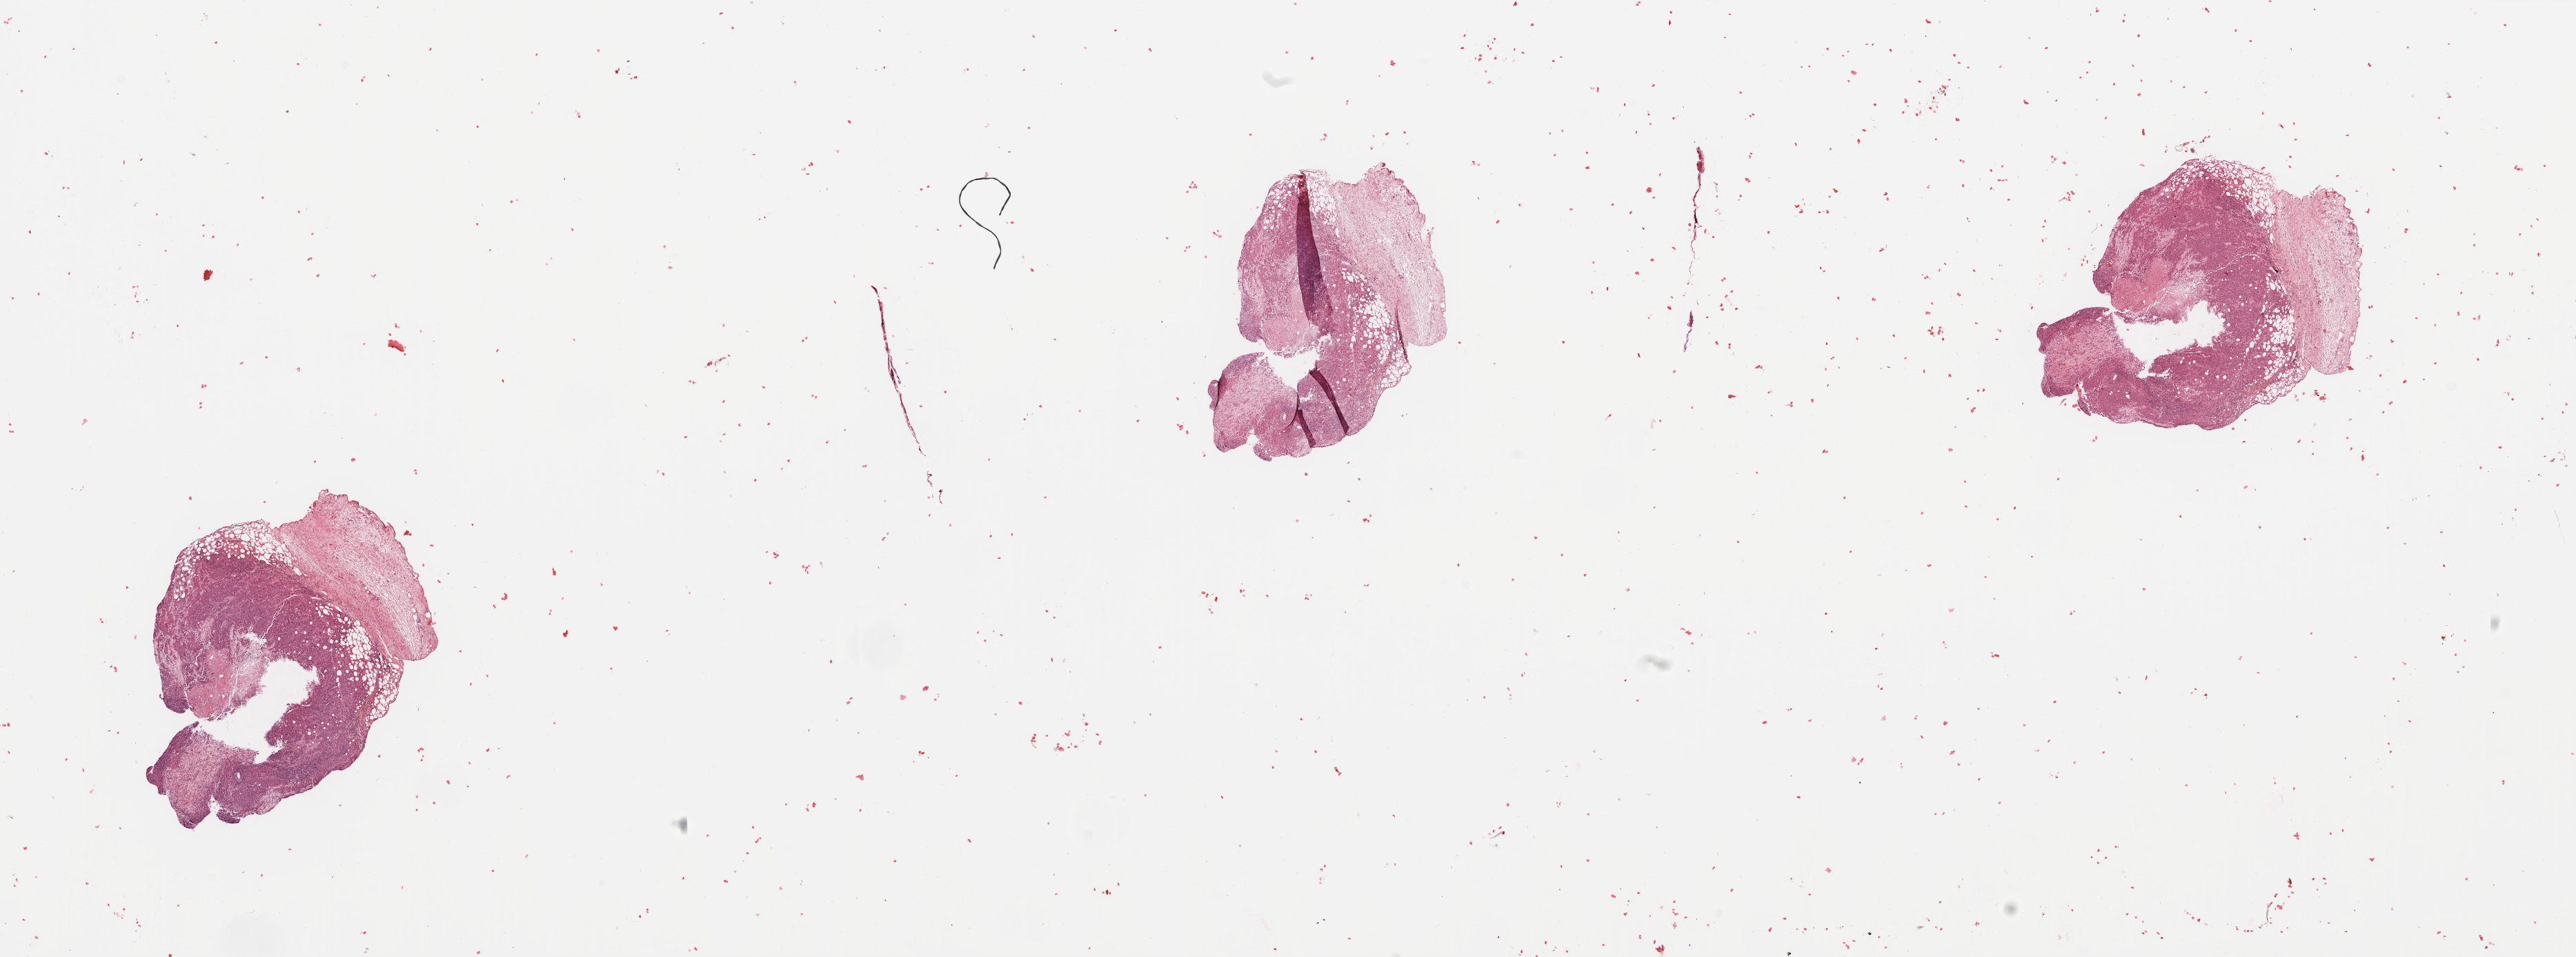
Digitized Hematoxylin and eosin (H&E) stained tissue section (whole slide), shown as a low-resolution overview of the whole scanned area (about 29.5 x 11.0 mm, acquisition: 20x scan). Pancreas, tumour tissue. Patient: female, age 61 years. Histologic grade: G3 (poorly differentiated).
Histologic diagnosis: Infiltrating duct carcinoma, NOS. Primary tumour site (as recorded): head. AJCC pathologic stage: III.